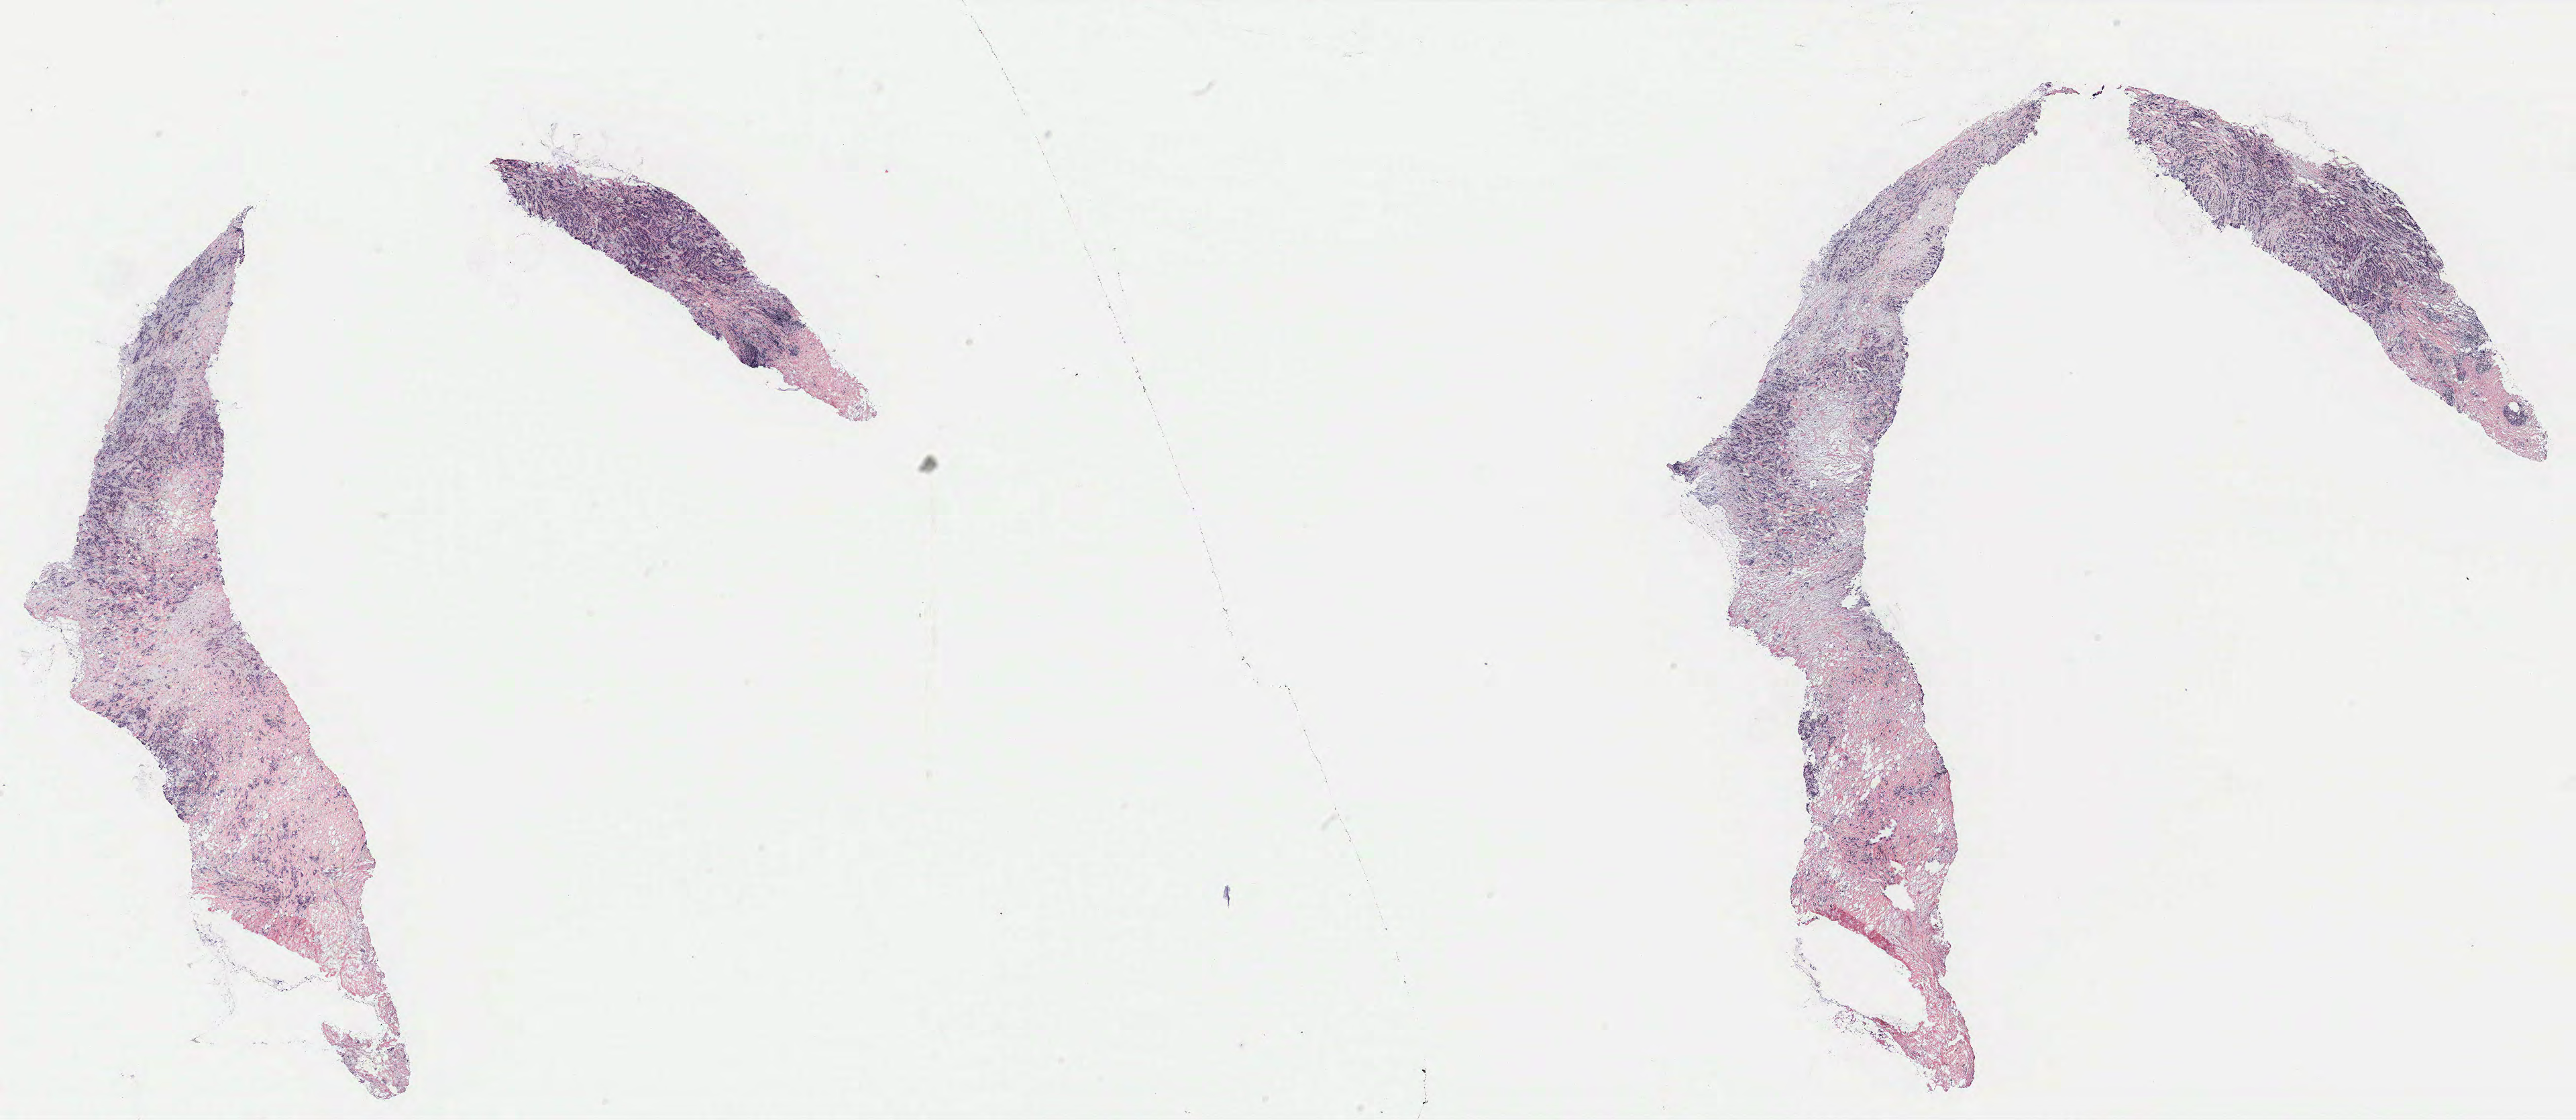
Hematoxylin and eosin (H&E) stained whole-slide image, a low-resolution overview of the entire scanned area, about 30.7 x 13.4 mm. Breast, tumour tissue. Patient: female, age 35 years.
AJCC pathologic stage: IIB. Histologic diagnosis: Infiltrating duct carcinoma, NOS.